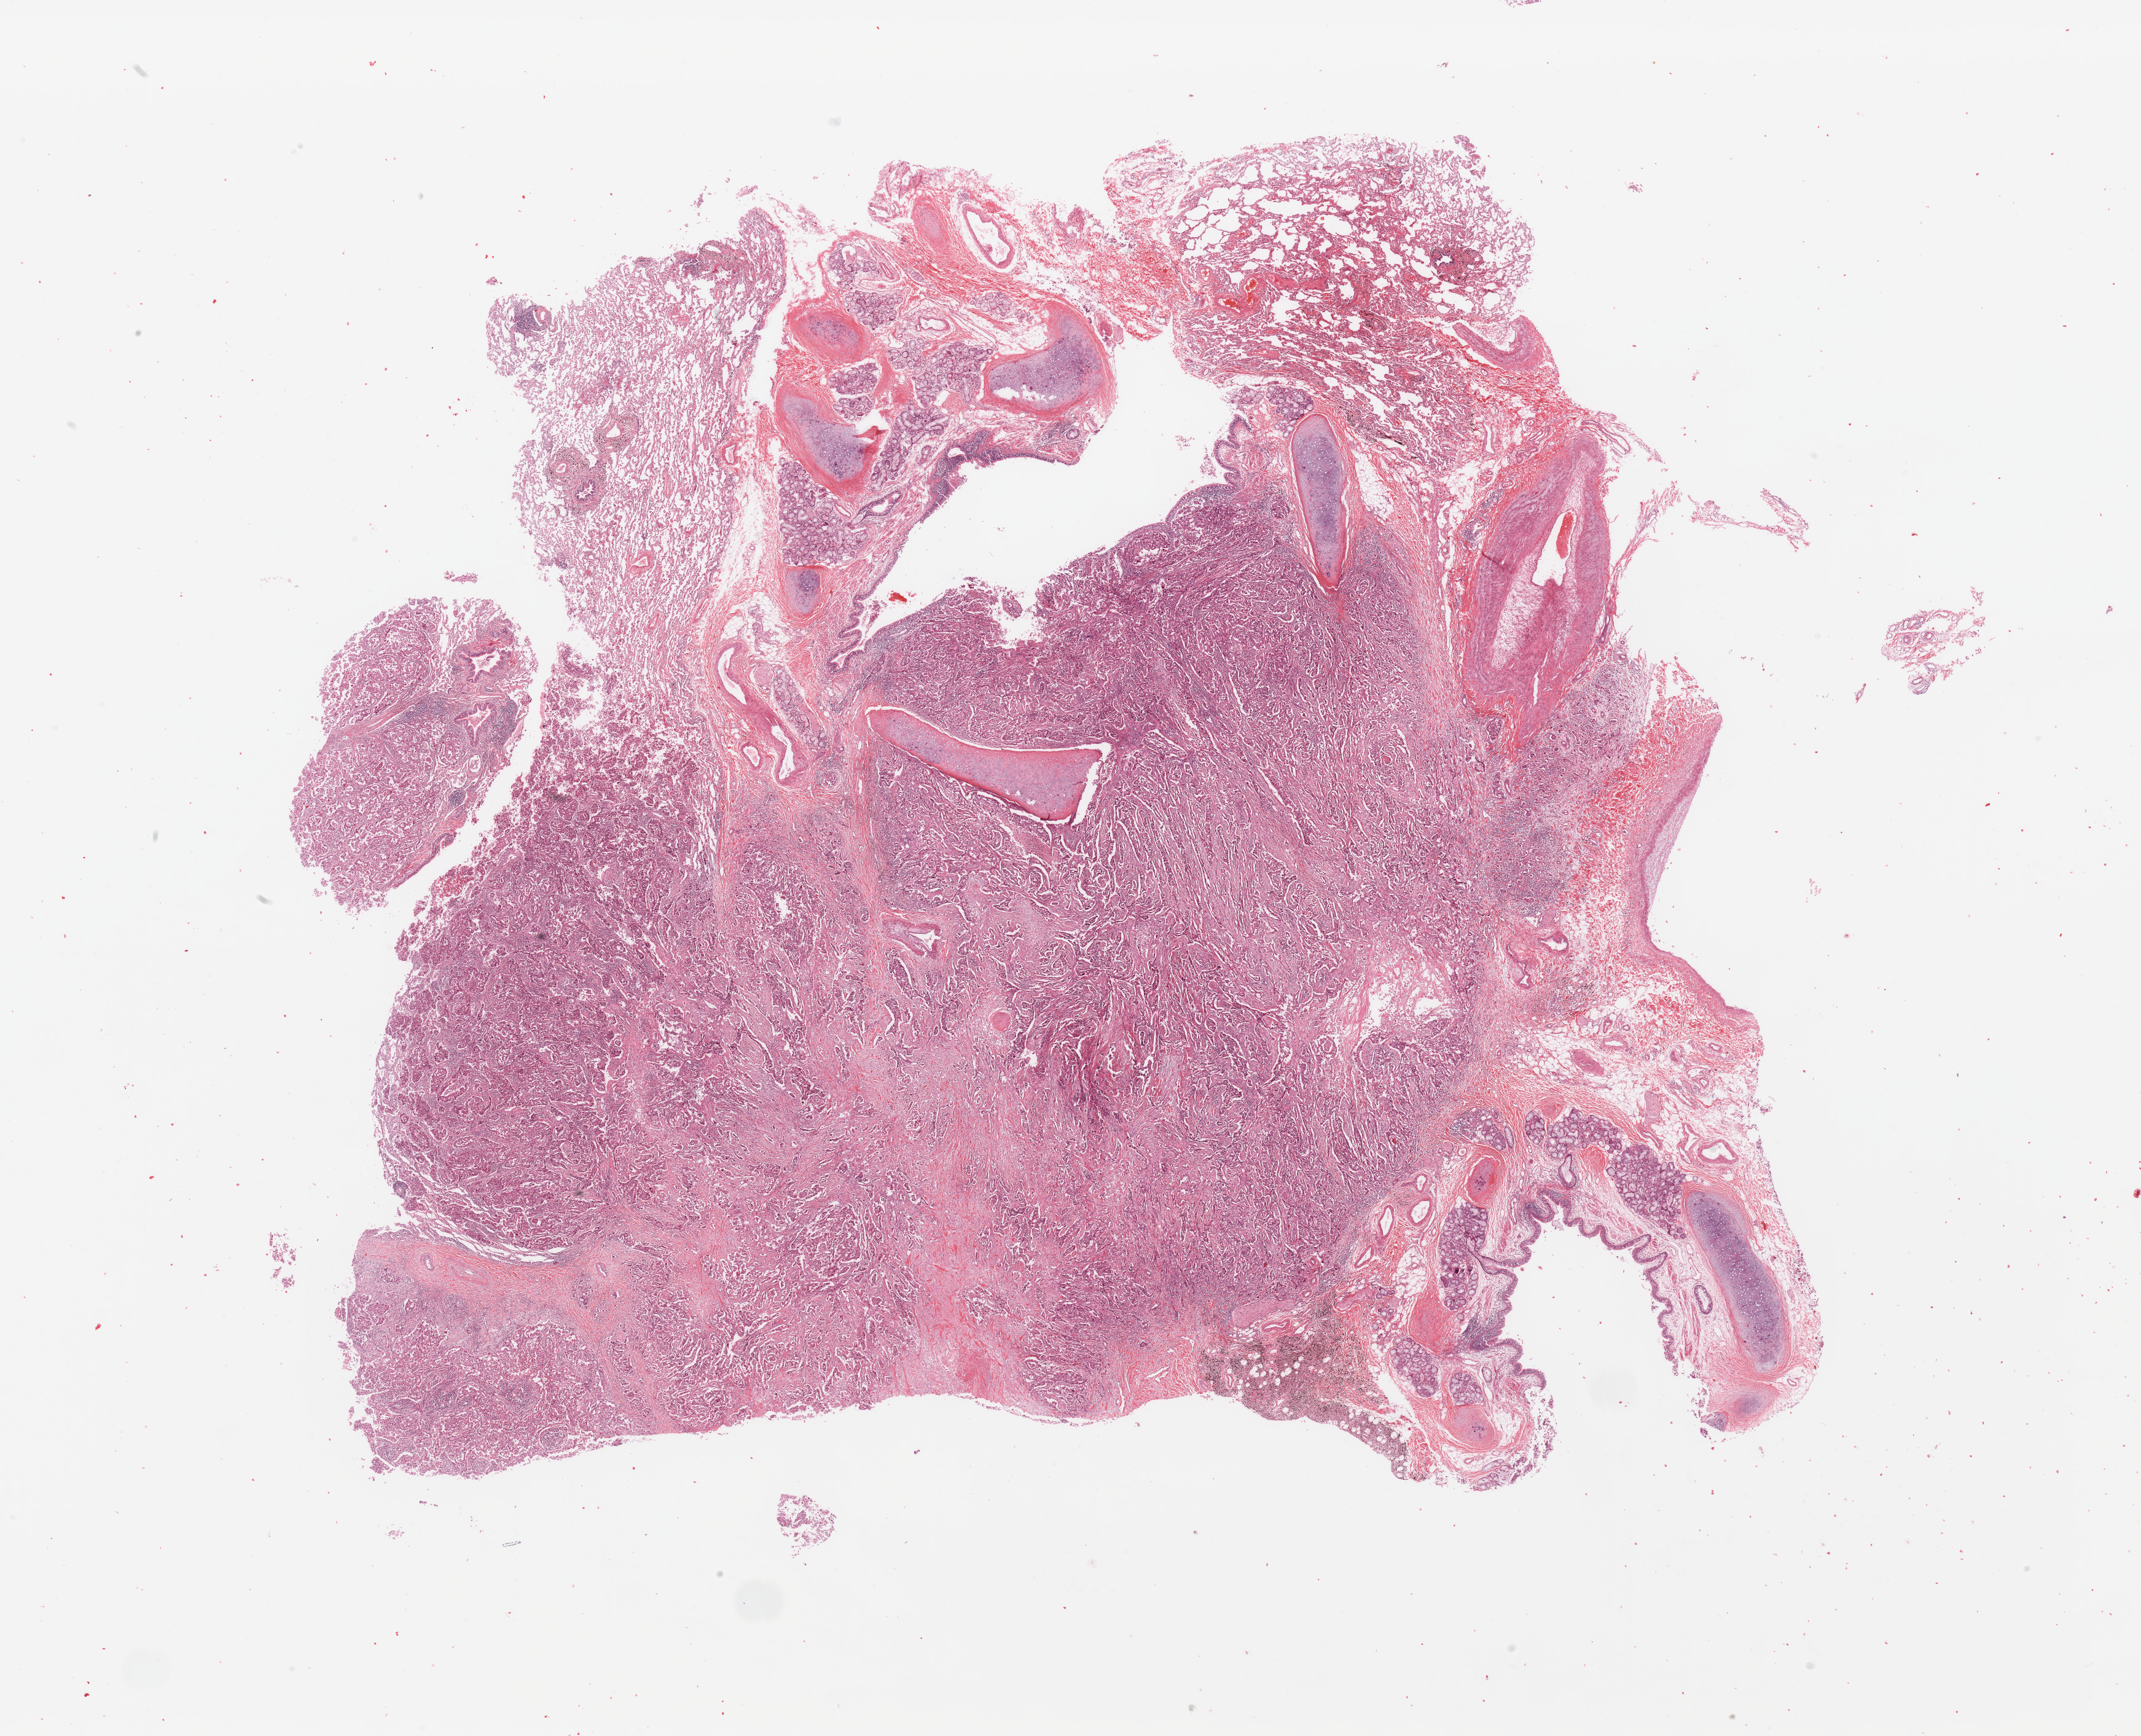
Whole-slide histology image, H&E-stained — a low-resolution overview of the entire scanned area, about 27.6 x 22.4 mm; tumour tissue sample, lung. Patient: female, age 61 years. Histologic grade: G3 (poorly differentiated).
AJCC pathologic stage: IIIA. Histologic diagnosis: Adenocarcinoma, NOS.